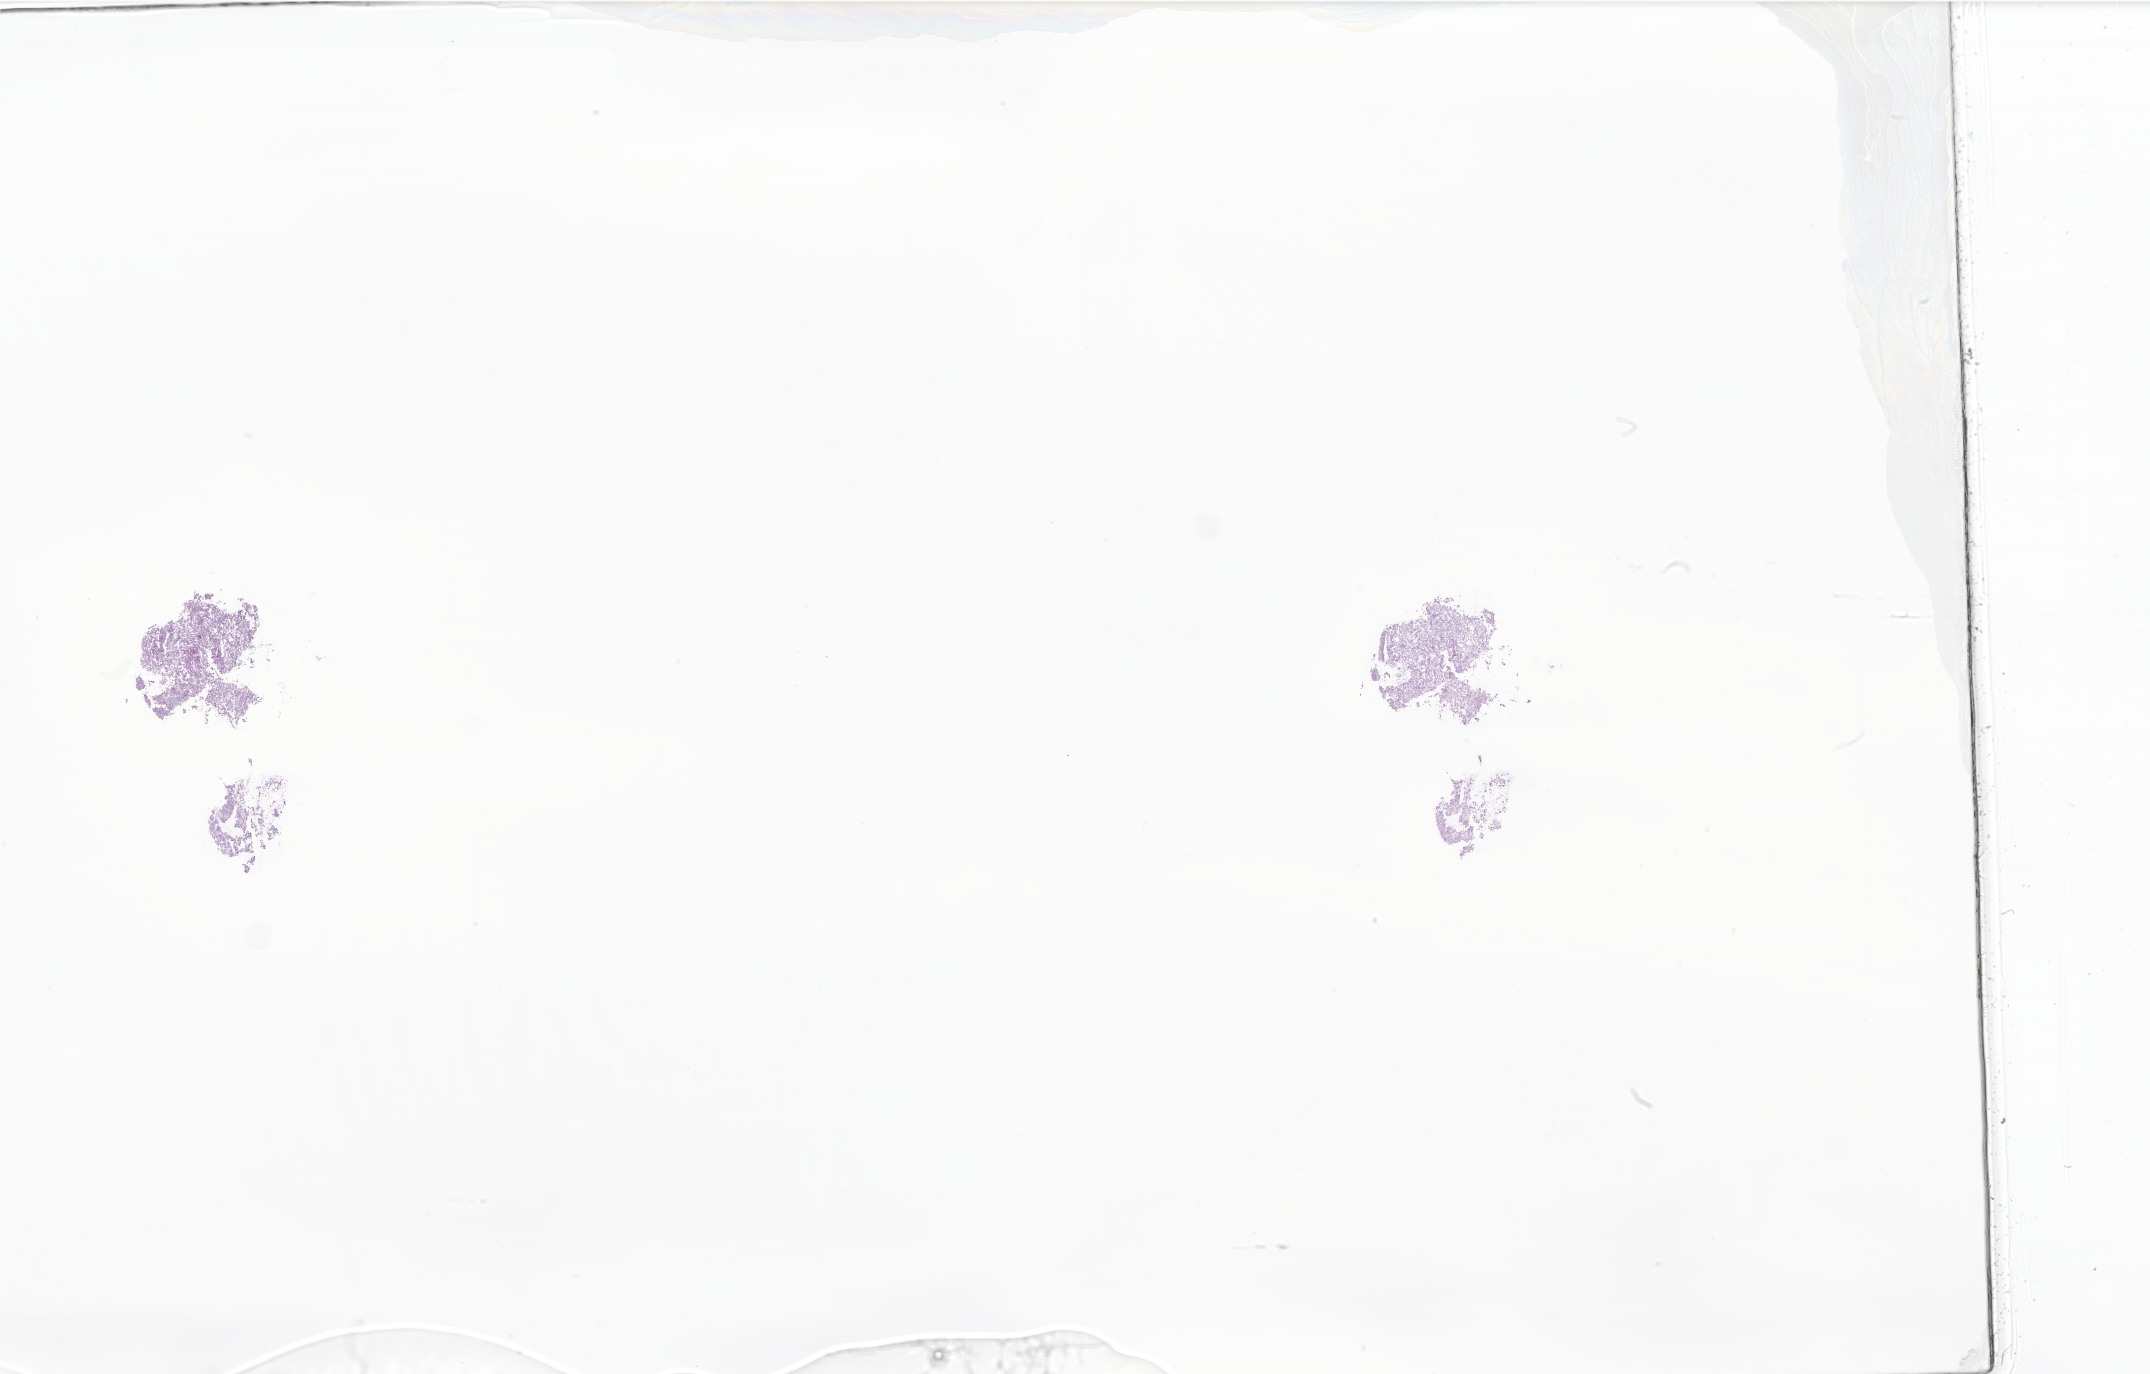
H&E whole-slide image of tumor tissue from the soft tissue of trunk, a low-resolution overview of the entire scanned area, about 36.3 x 23.2 mm; frozen section. Female patient, age 165 months.
Diagnosis (ICD-O-3 morphology term): Sarcoma, NOS.